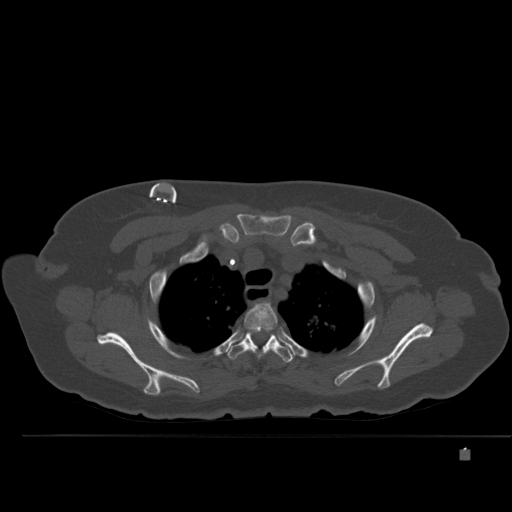
CT including the spine, one axial slice; position 385 of 477 along the scan axis; bone window (W 1800 / L 400 HU); 512 × 512 image matrix, field of view 422 × 422 mm. Patient: female, 74 years. Case-level facts recorded for this patient, not image findings: primary cancer: colon.
Structures marked on this image (semi-automatically segmented with operator editing):
- T2 vertebra: bounding box [x1, y1, x2, y2] px = [243, 303, 278, 355]
- T3 vertebra: [227, 328, 295, 363]